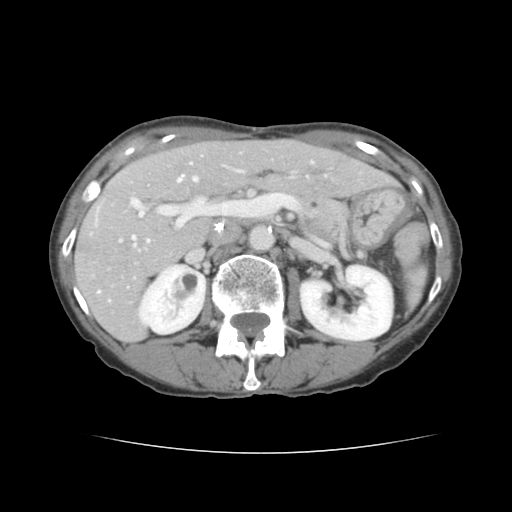
Contrast-enhanced abdominal CT, one axial slice. Position 74 of 136 along the scan axis. Intravenous contrast given. Soft-tissue window (W 400 / L 40 HU). 2.5 mm slice thickness. 512 × 512 image matrix. Female patient, age 77 years. Case-level facts recorded for this patient, not image findings: diagnosis: colorectal cancer liver metastases, imaged before liver resection; multiple liver metastases: yes; largest metastasis: 3 cm; disease in both lobes: no.
Structures marked on this image (expert manual segmentation):
- hepatic veins: bounding box (x1, y1, x2, y2) in pixels: (132, 175, 197, 239)
- liver: (75, 141, 390, 340)
- planned liver remnant (the part of the liver to remain after resection): (156, 141, 391, 199)
- portal vein (with intrahepatic branches): (98, 170, 242, 293)